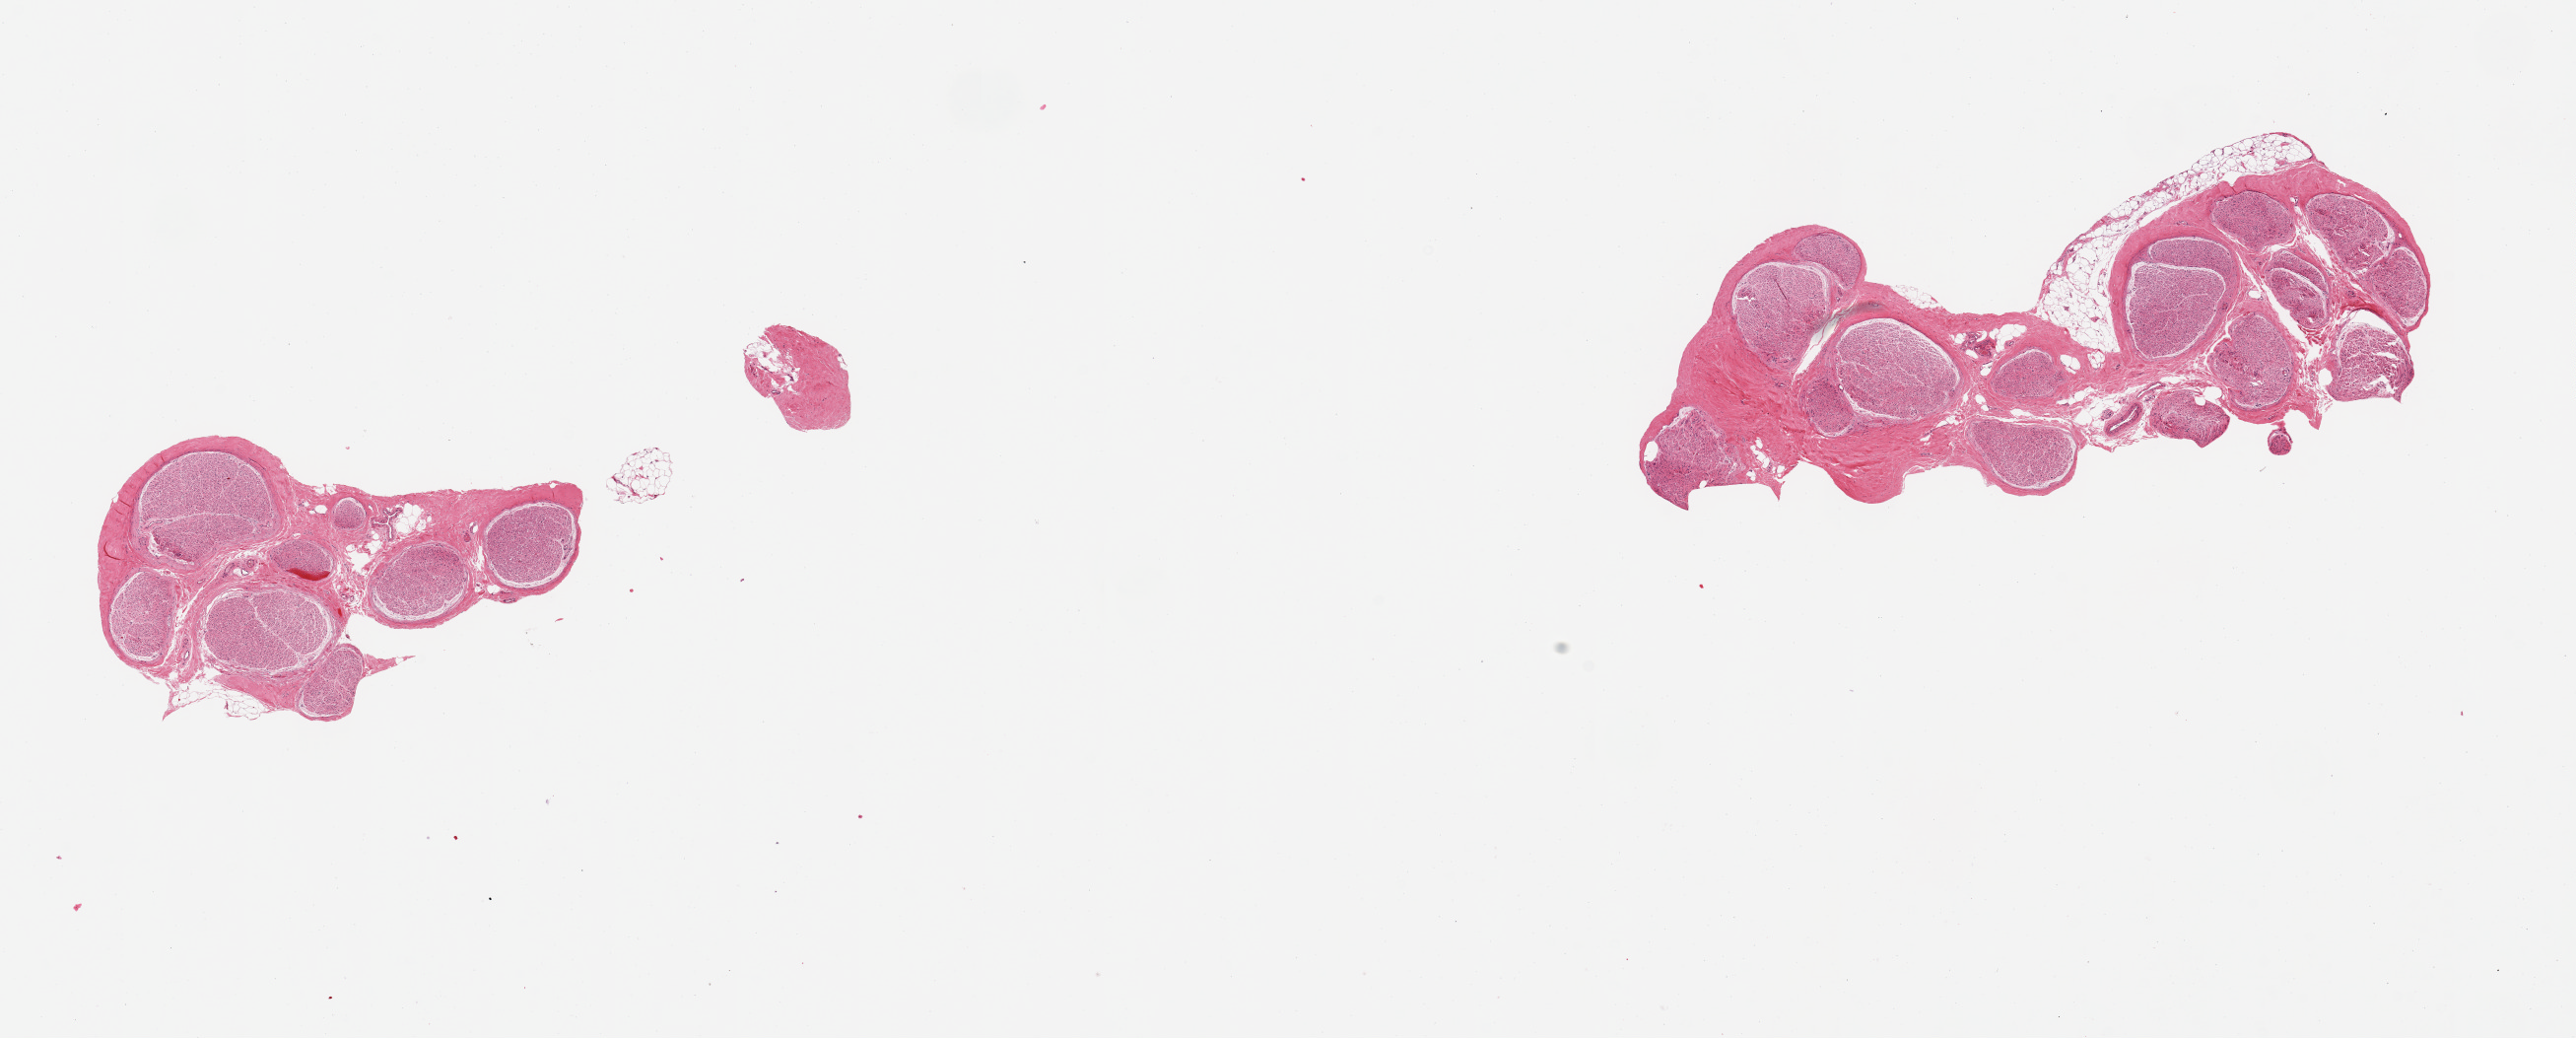
Hematoxylin and eosin (H&E) whole-slide image, a low-resolution overview of the entire scanned area, about 20.7 x 8.3 mm (slide scanned at 20x). PAXgene-fixed paraffin-embedded (PFPE) section. Section of tibial nerve (target tissue). Donor tissue sample.
Review note (as recorded): 2 pieces; relatively well trimmed, small portion of attached fat on one piece.